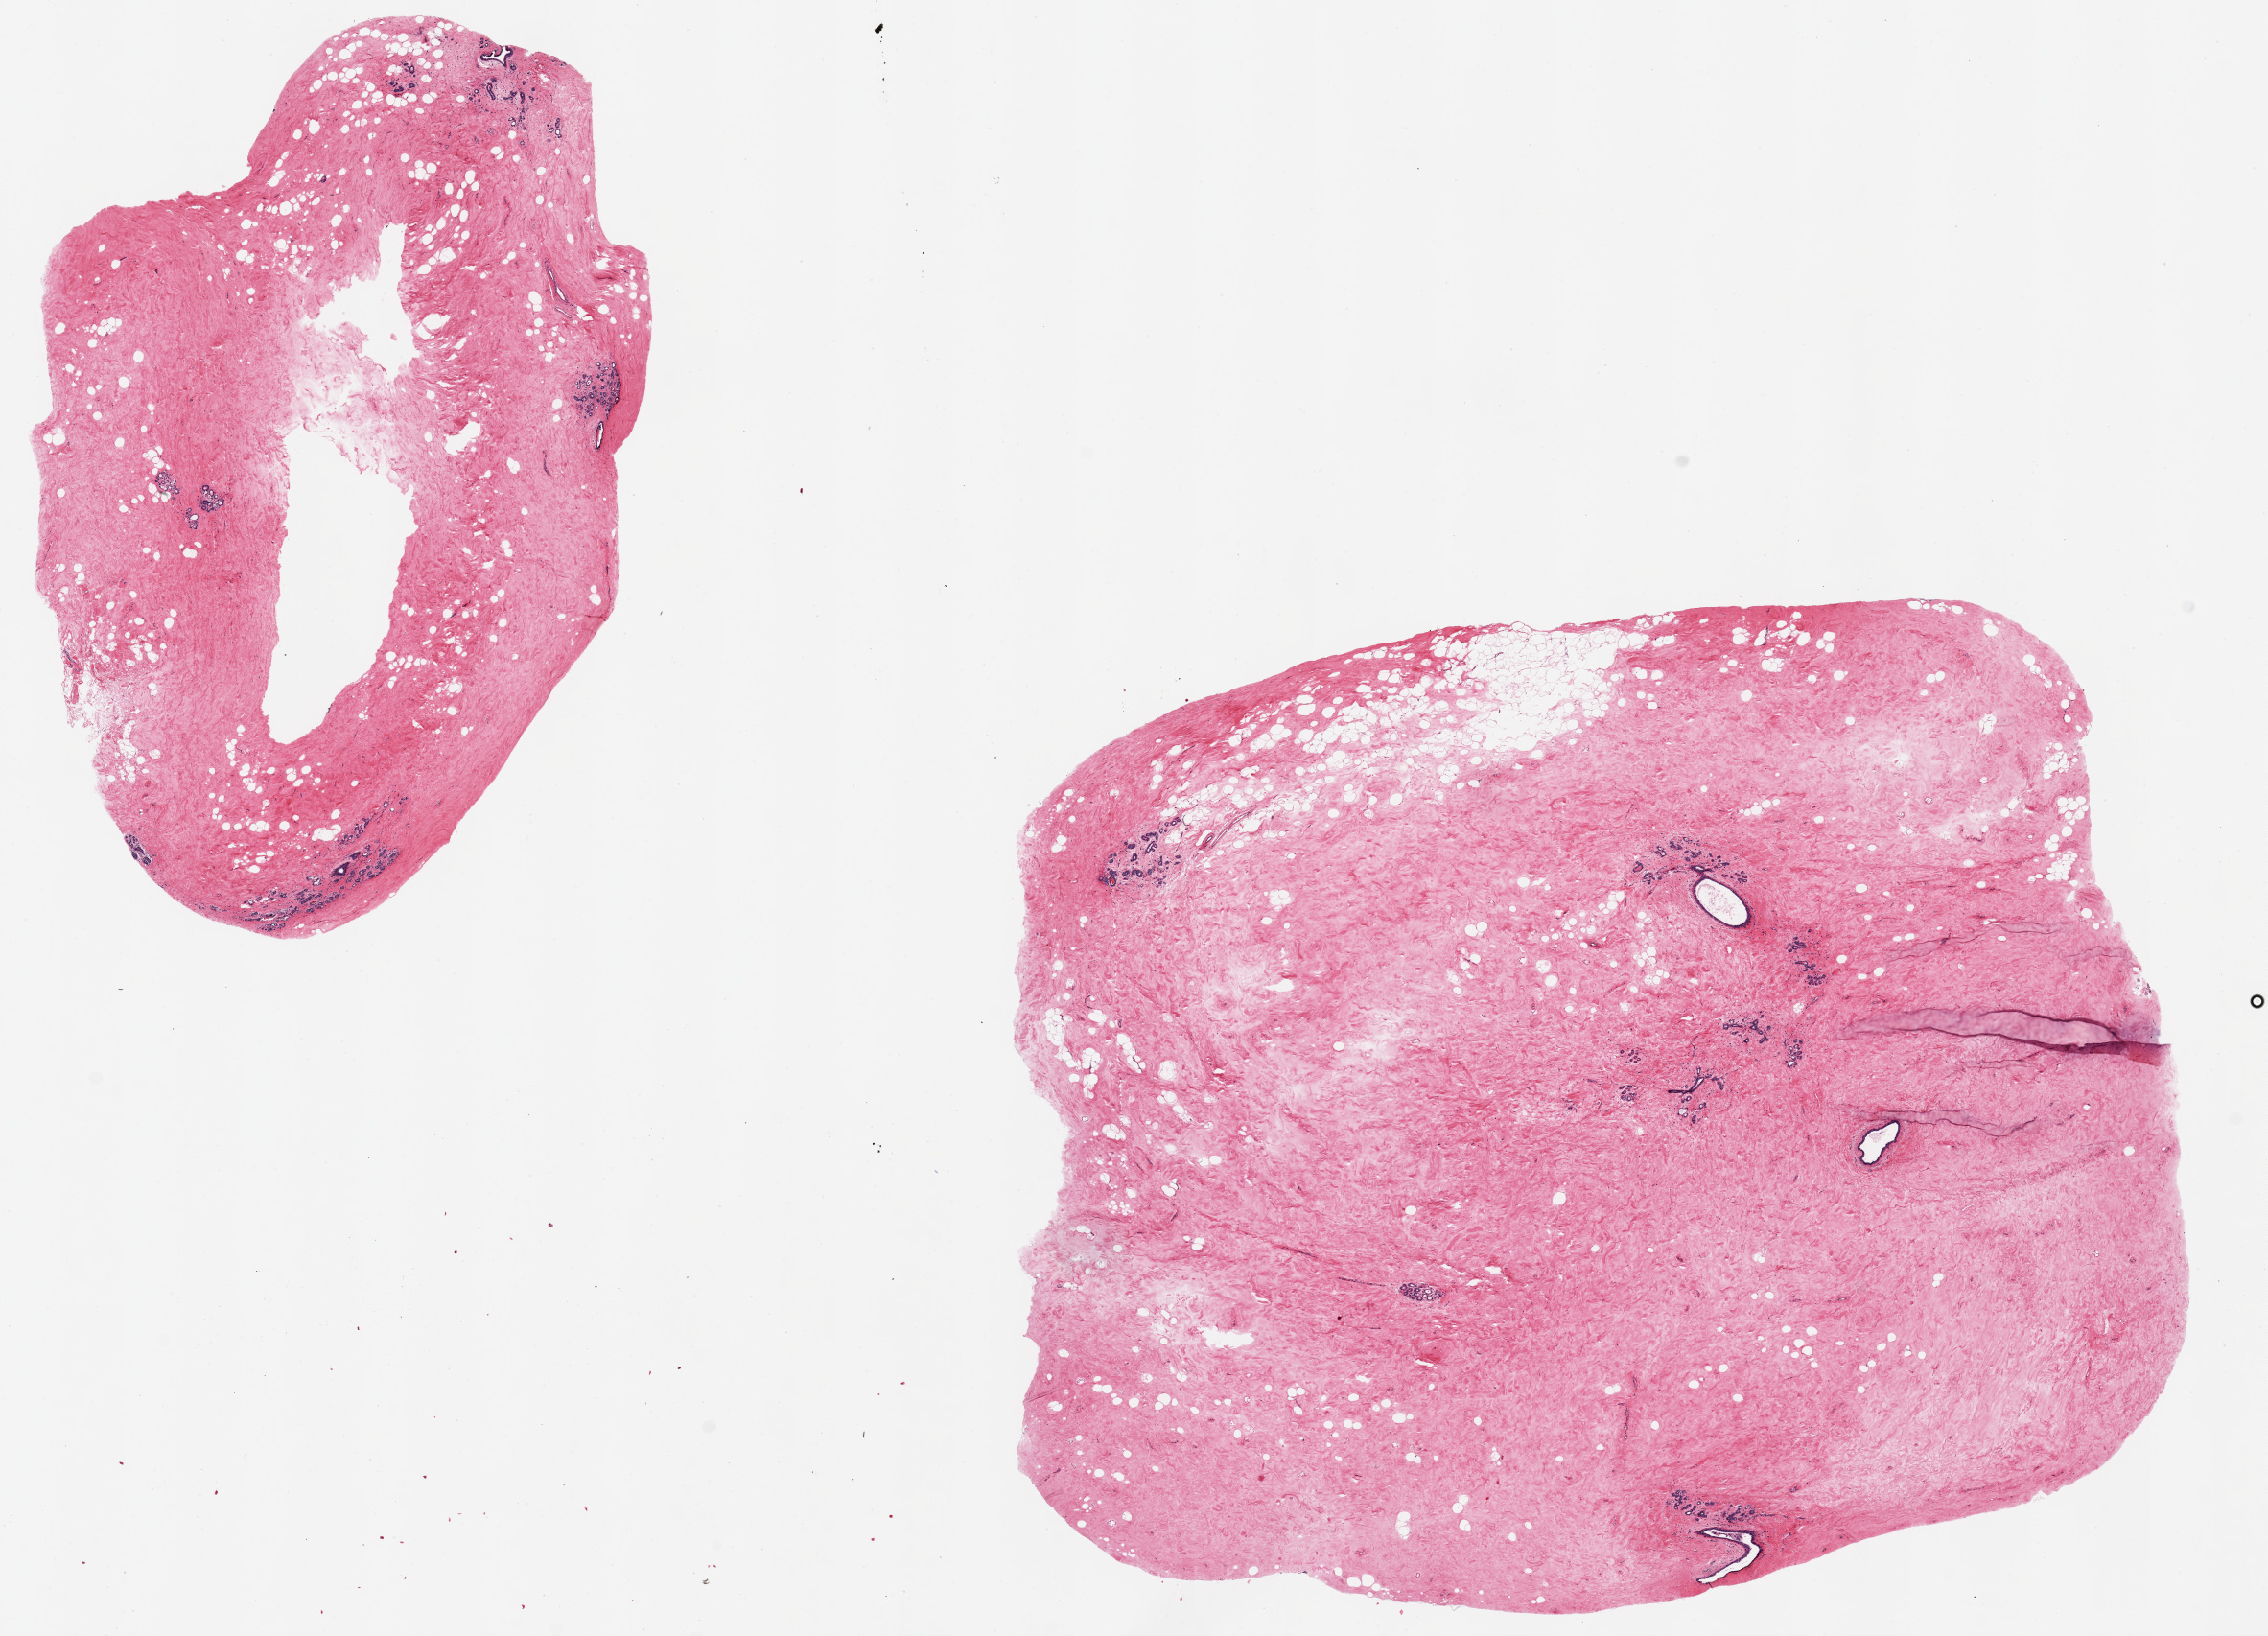
Haematoxylin and eosin whole-slide image, brightfield — low-resolution overview of the scanned area, about 18.7 x 13.5 mm (acquisition: 20x scan). PAXgene-fixed paraffin-embedded (PFPE) section. Target tissue: breast. Tissue donor sample. Donor: female.
Review note (as recorded): 2 pieces, 8x5 & 10x8mm; fibrous stroma, rare atrophic TDLUs present.